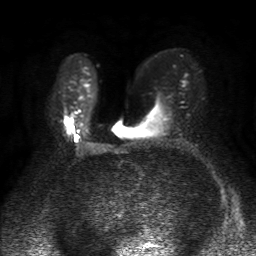
Breast MRI, one axial slice; diffusion-weighted series; image 2 of 4 stored at this slice position (different b-values; order by instance number); 1.5 T; 4 mm slice thickness; 256 × 256 image matrix, field of view 320 × 320 mm. Female patient.
Structures marked on this image (expert manual segmentation):
- tumour on diffusion-weighted imaging: bounding box (x1, y1, x2, y2) in pixels: (65, 118, 72, 126)